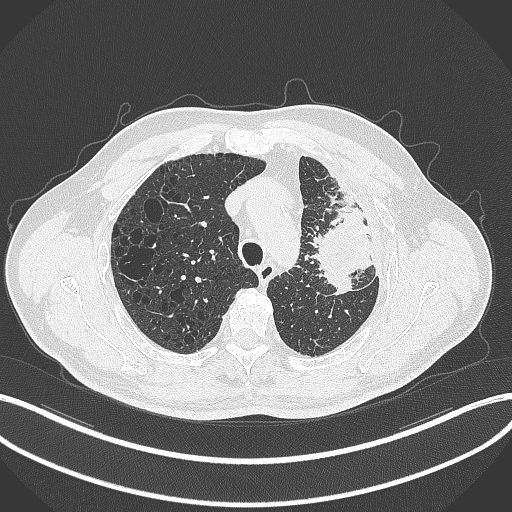
Chest CT, one axial slice. Slice 246 of 297 in the series (ordered by position). 120 kVp. Lung window (W 1500 / L -600 HU). 1 mm slice thickness. 512 × 512 image matrix. Male patient, age 68 years. Case-level facts recorded for this patient, not image findings: clinical TNM (as recorded): T3 N3 M1.
Outlined on this slice (rectangle marked by the reading radiologist):
- lung tumour (recorded histology: adenocarcinoma): bounding box (x1, y1, x2, y2) in pixels: (315, 196, 376, 296)